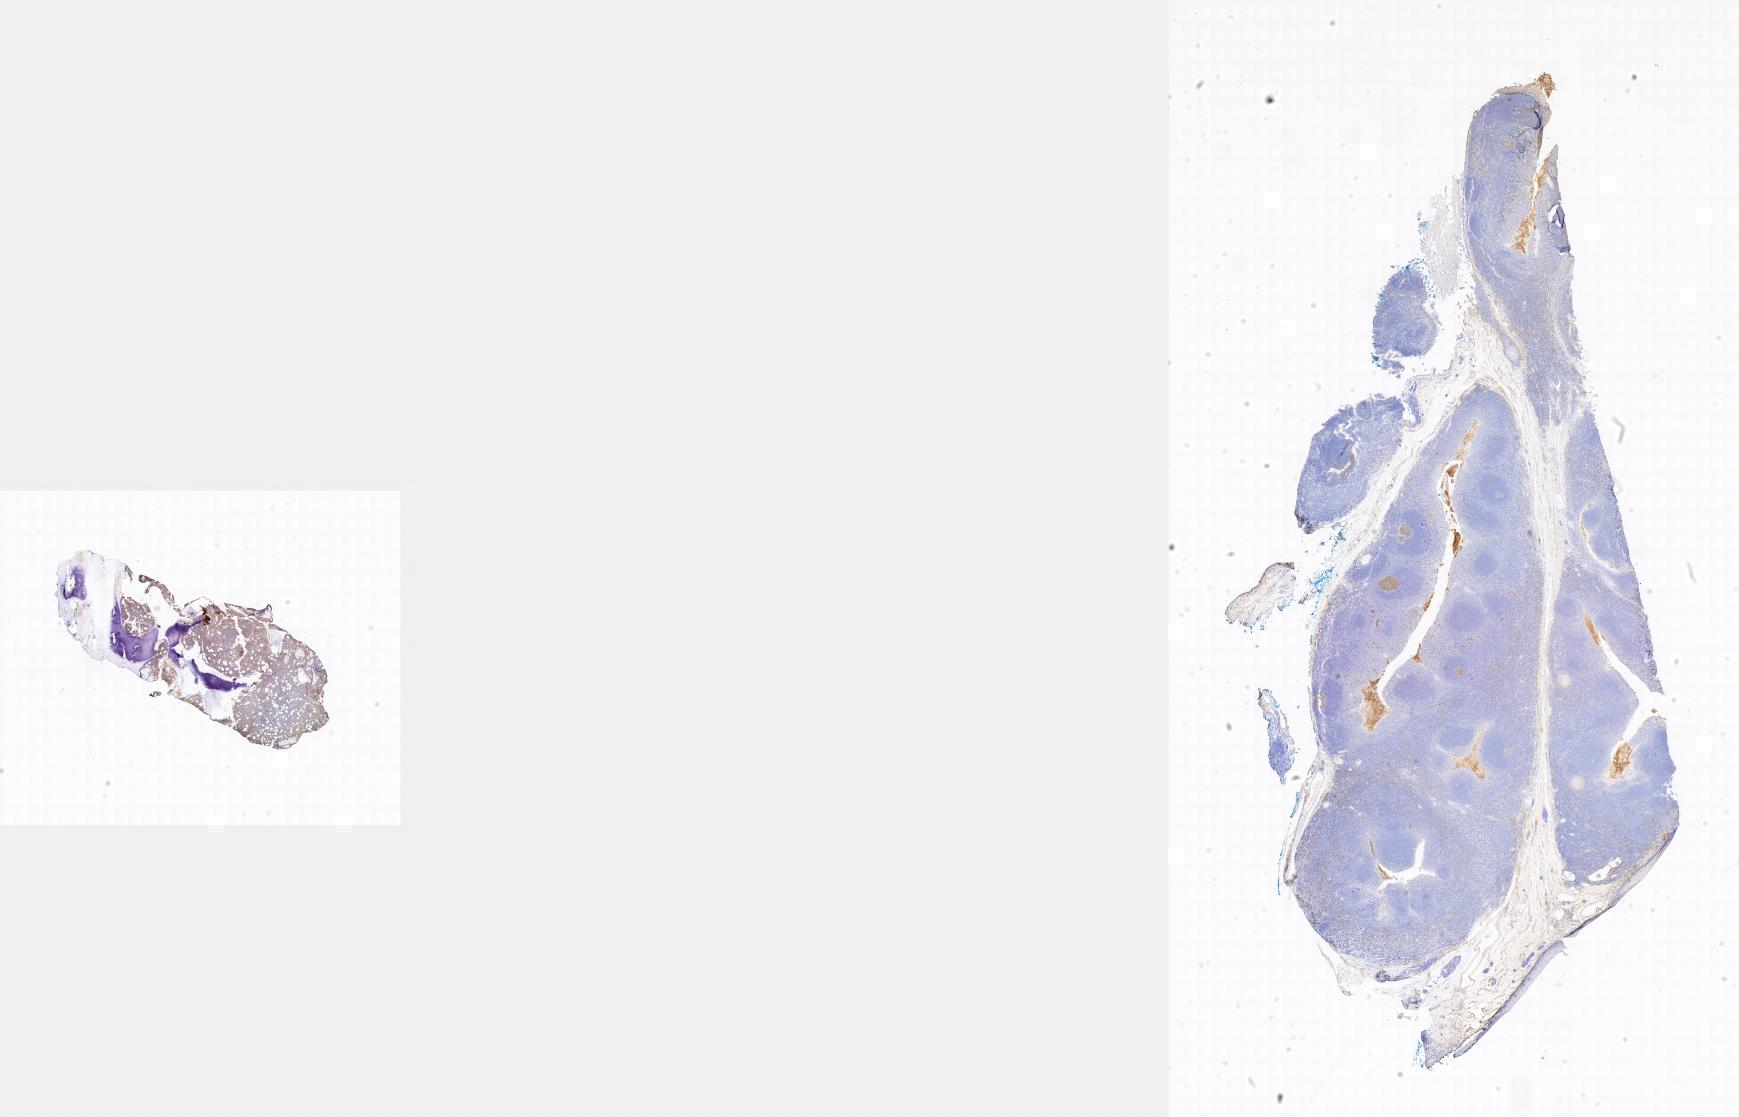
Whole-slide image, immunohistochemical stain for CD10 — whole scanned area shown as a low-resolution overview; specimen: tumor tissue; anatomic site: bone marrow. Patient male; 15 years old.
Histologic diagnosis: Burkitt lymphoma, NOS.